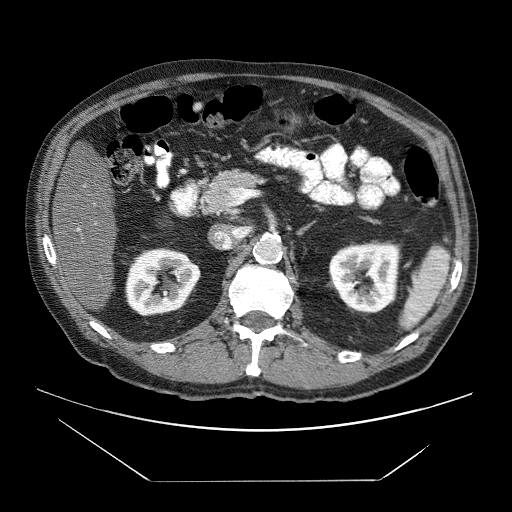
Contrast-enhanced abdominal CT (liver protocol), one axial slice; slice 22 of 83 in the series (ordered by position); 120 kVp; soft-tissue window (W 400 / L 40 HU); 2.5 mm slice thickness; 512 × 512 image matrix, field of view 420 × 420 mm. From the clinical record (not read from this slice): diagnosis: hepatocellular carcinoma (patient treated with transarterial chemoembolisation; whether this scan precedes or follows treatment is not stated here); TNM stage (as recorded): Stage-IVB; Child-Pugh class: B.
Outlined on this slice (semi-automatically segmented with operator editing):
- liver parenchyma outside the tumour (the mass and vessels are separate outlines, so this box may not span the whole liver): bounding box [x1, y1, x2, y2] px = [52, 157, 116, 308]
- liver vessels: [77, 228, 80, 231]